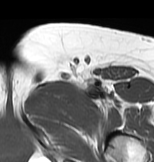
MRI of an extremity soft-tissue mass, one axial slice. MR volume resampled by the dataset authors to the PET/CT grid (not the native acquisition matrix). 154 × 162 image matrix, field of view 150 × 158 mm. Female patient. Case-level facts recorded for this patient, not image findings: histological type: myxofibrosarcoma; grade: intermediate; site of the primary tumour: left thigh.
Structures marked on this image (expert contour drawn on MRI and transferred to this co-registered scan by the dataset authors):
- gross tumour volume including surrounding oedema: bounding box [x1, y1, x2, y2] px = [30, 75, 120, 115]